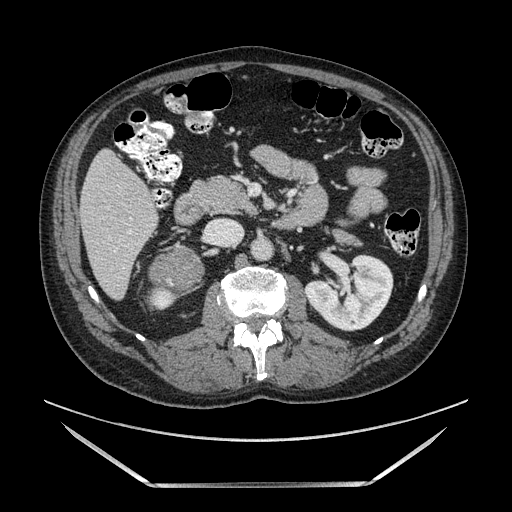
Contrast-enhanced abdominal CT, one axial slice; slice 52 of 185 in the series (ordered by position); soft-tissue window (W 400 / L 40 HU); 1.25 mm slice thickness; 512 × 512 image matrix, field of view 440 × 440 mm. Male patient. Case-level facts recorded for this patient, not image findings: diagnosis: adrenocortical carcinoma; tumour side: right adrenal; tumour size at pathology: 10.3 cm; Ki-67 index: 20 %; stage (as recorded): 3.
Outlined on this slice (semi-automatic segmentation, software-assisted and operator-edited):
- mass: bounding box [x1, y1, x2, y2] px = [153, 245, 201, 290]